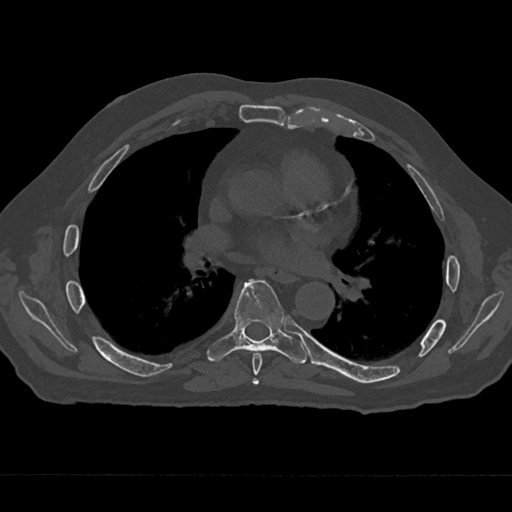
CT including the spine, one axial slice. Slice 383 of 797 in the series (ordered by position). Reconstruction kernel Br40s/3. Bone window (W 1800 / L 400 HU). 512 × 512 image matrix, field of view 377 × 377 mm. Male patient, age 75 years. From the clinical record (not read from this slice): primary cancer: renal; vertebrae with lytic lesions (as recorded): T4.
Annotated regions visible in this slice (semi-automatic segmentation, software-assisted and operator-edited):
- T6 vertebra: bounding box <252,352,263,385> (left, top, right, bottom; pixels)
- T7 vertebra: <207,279,307,364>